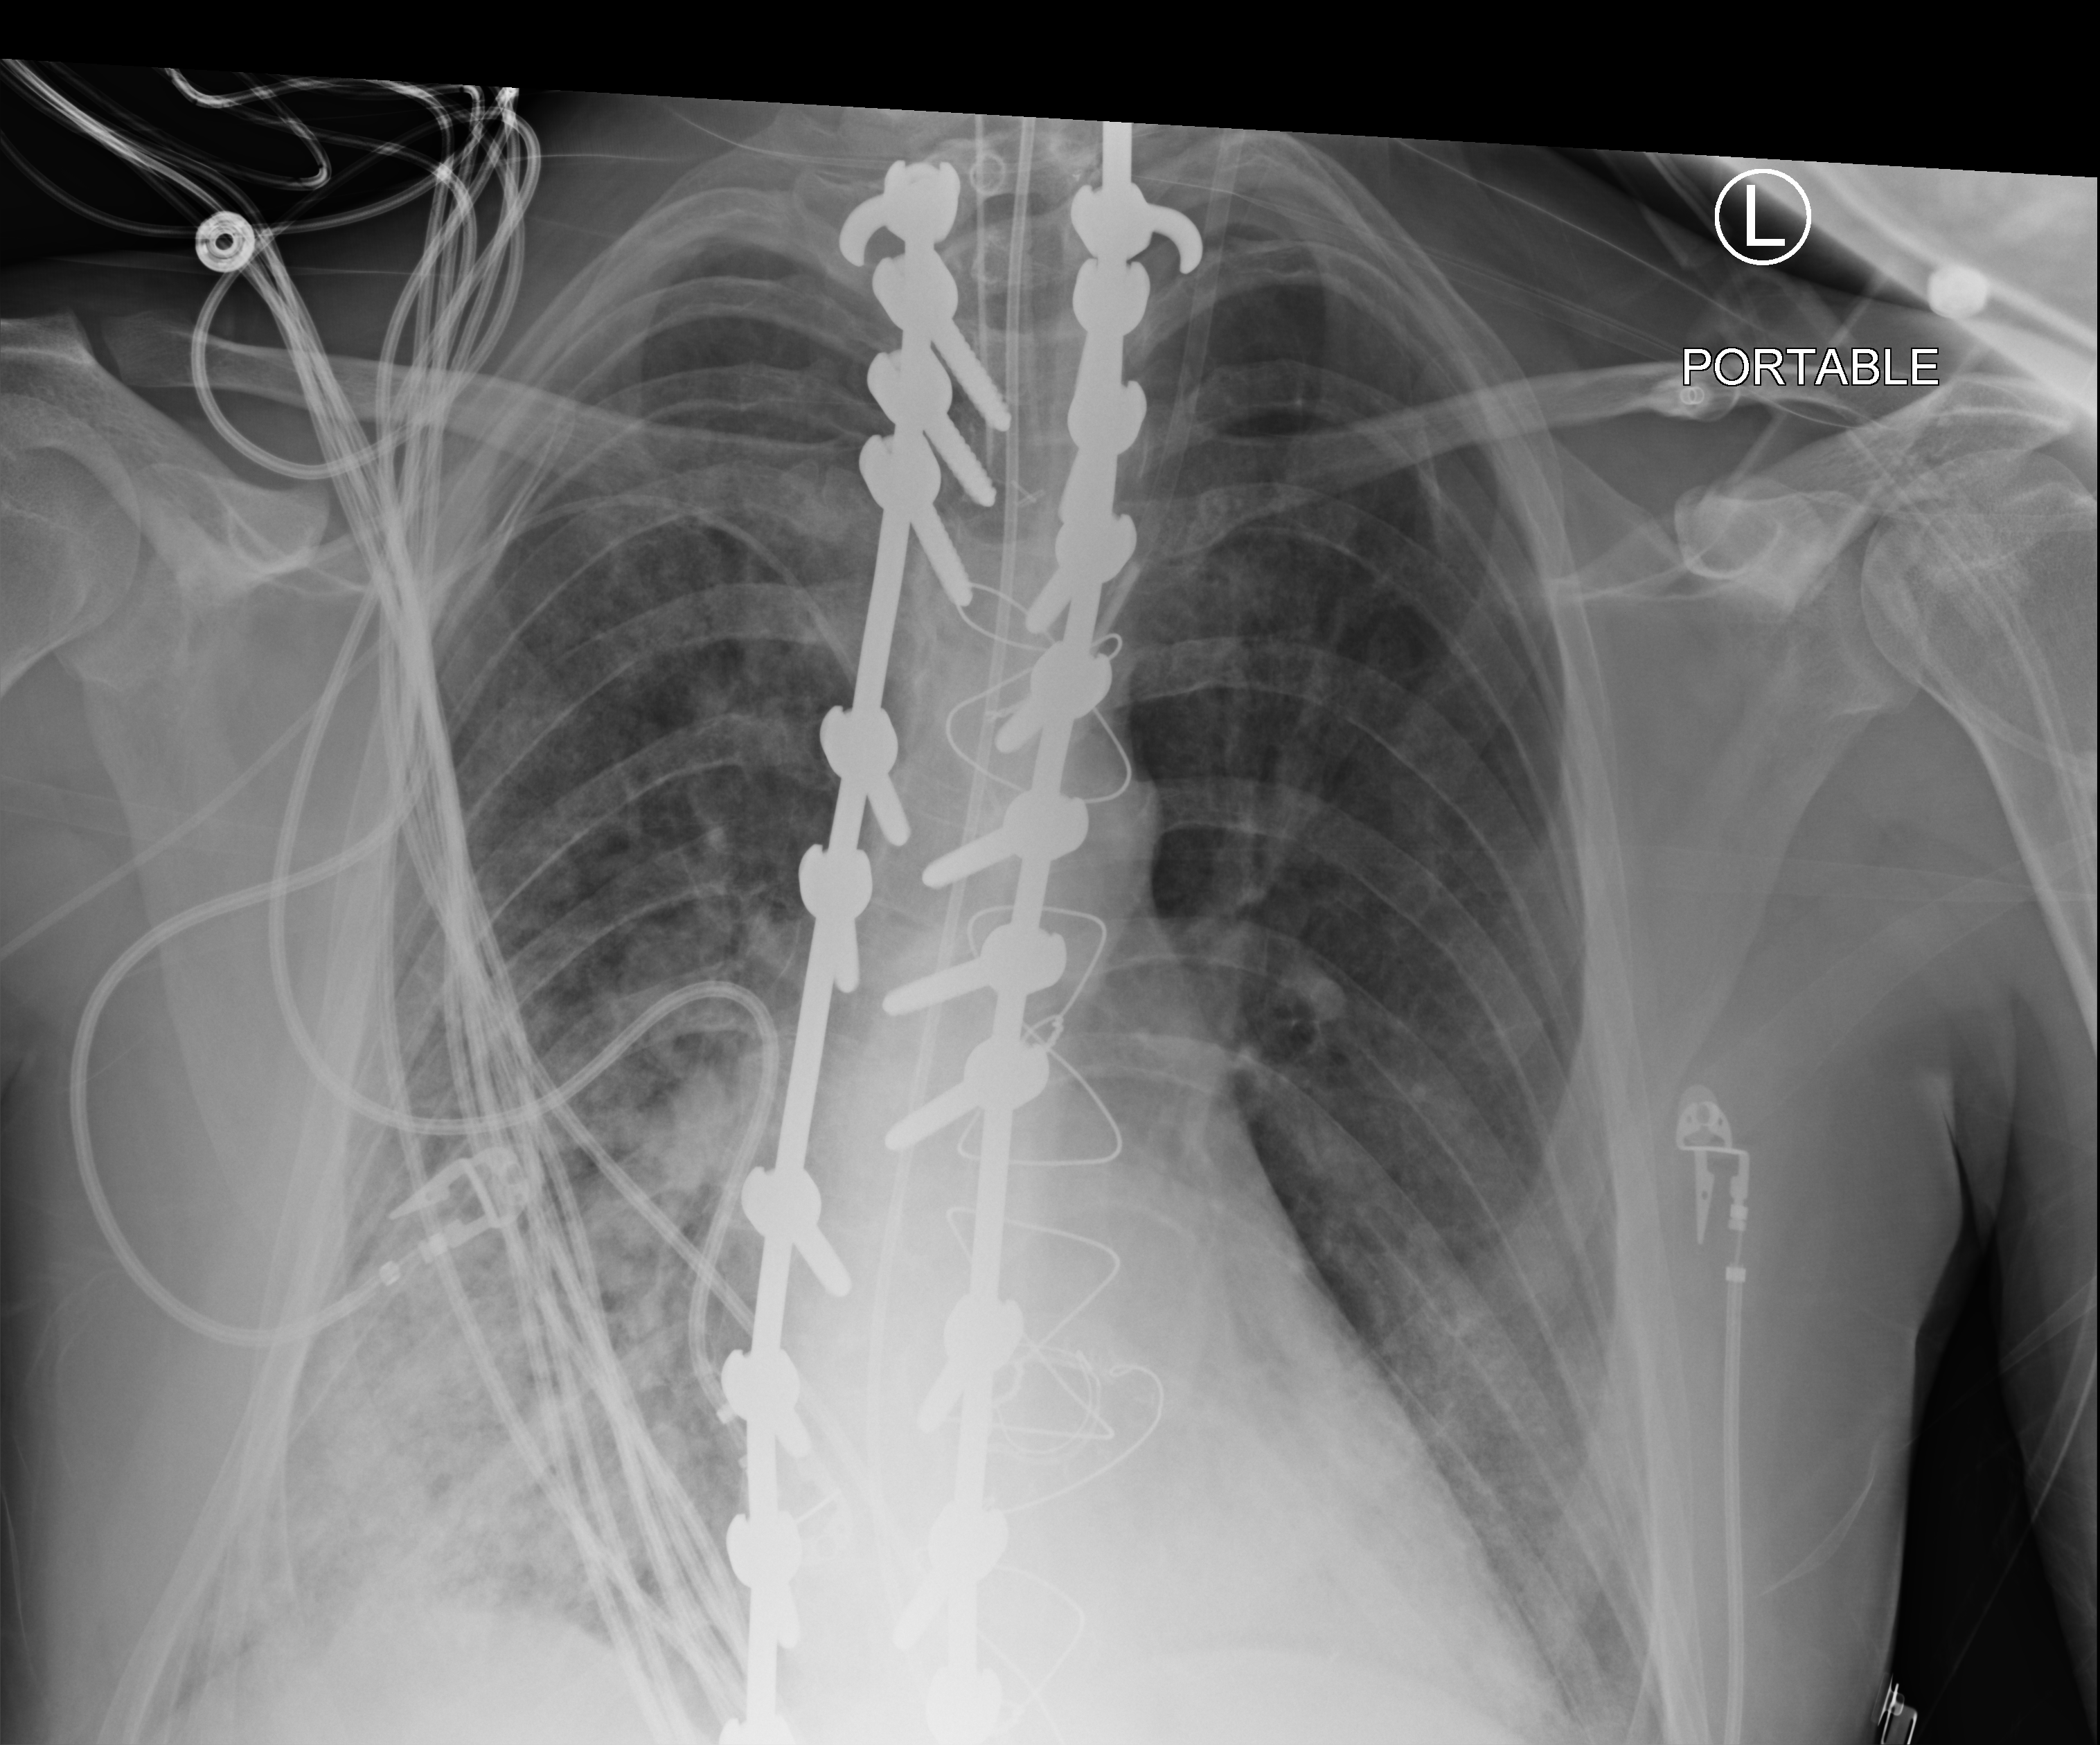
Chest X-ray (portable); anteroposterior (AP) projection. Adult patient hospitalised with COVID-19, age 18–59 years.
Admission-level facts for this patient (not findings on this image; timing relative to this image not recorded):
- mechanically ventilated during this hospital stay: yes